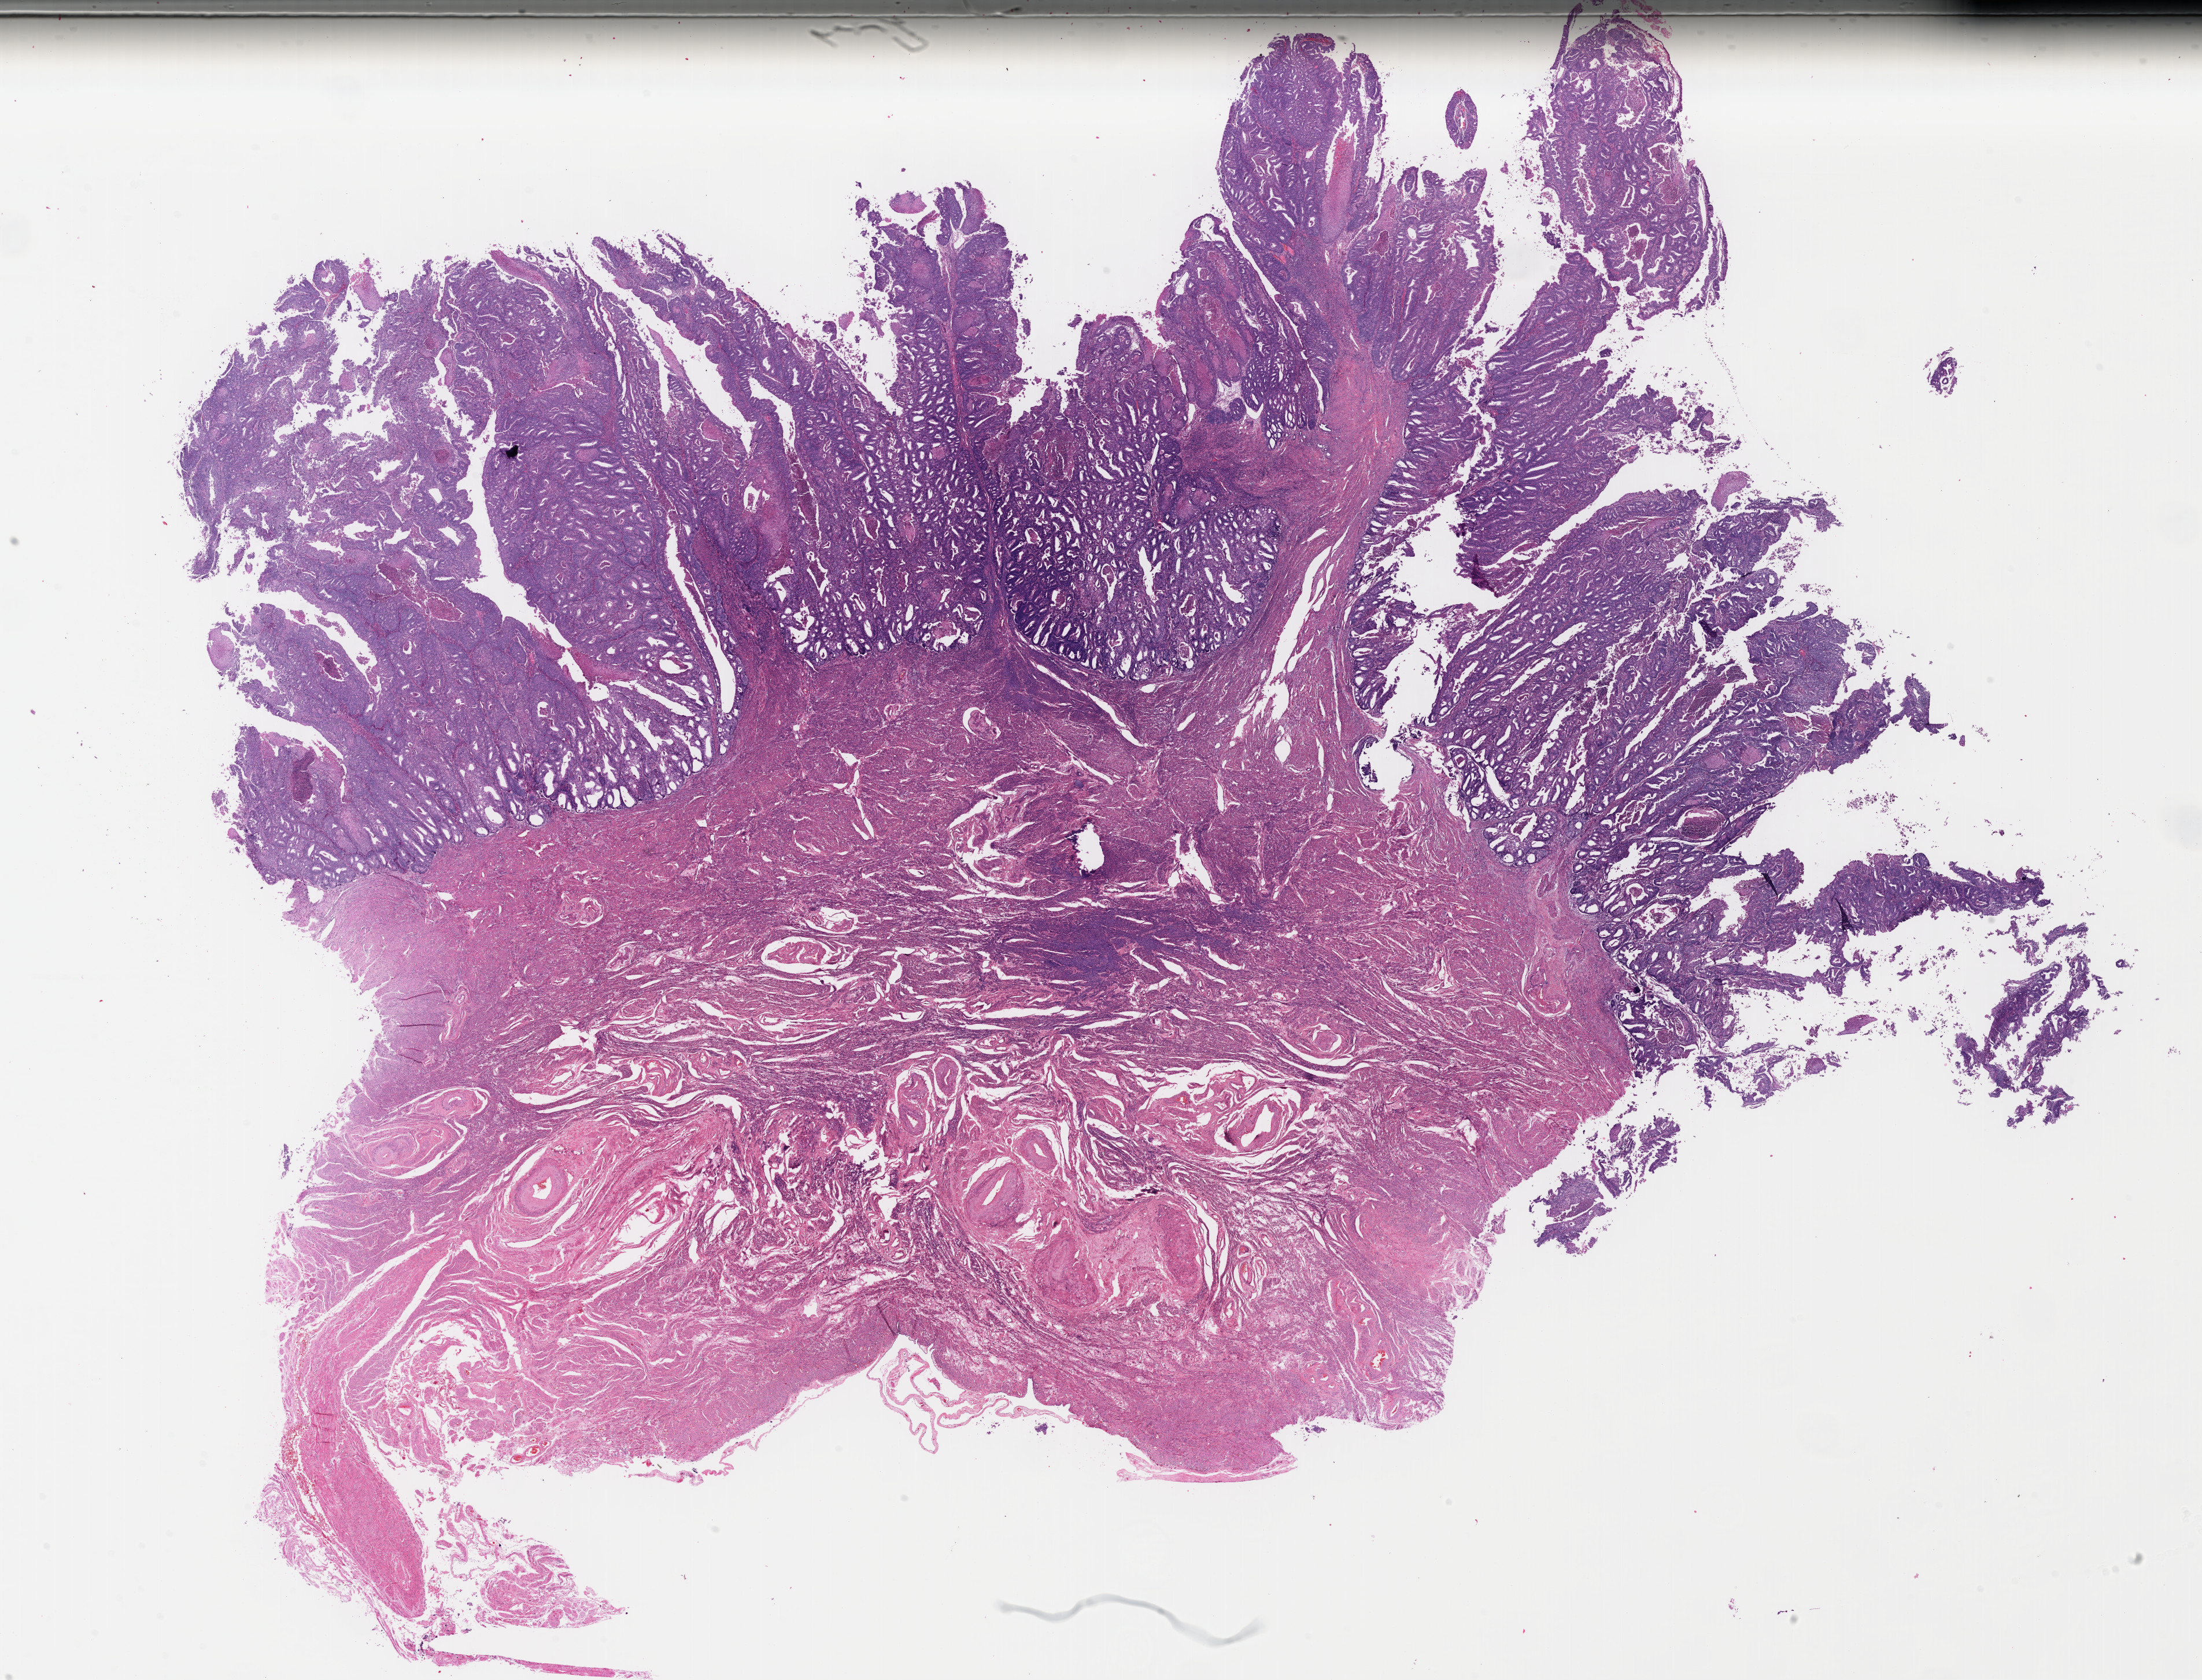
Whole-slide histology image, H&E — whole scanned area (about 29.9 x 22.8 mm, acquisition: 40x scan) shown as a low-resolution overview, formalin-fixed paraffin-embedded (FFPE) diagnostic section, sample: primary tumour, uterus. Patient: female, age at initial diagnosis 84 years. Histologic grade: G2 (moderately differentiated).
- pathologic diagnosis: Endometrioid adenocarcinoma, NOS (endometrium)
- lymph nodes positive (case pathology): 0 of 19 examined
- FIGO stage: IA